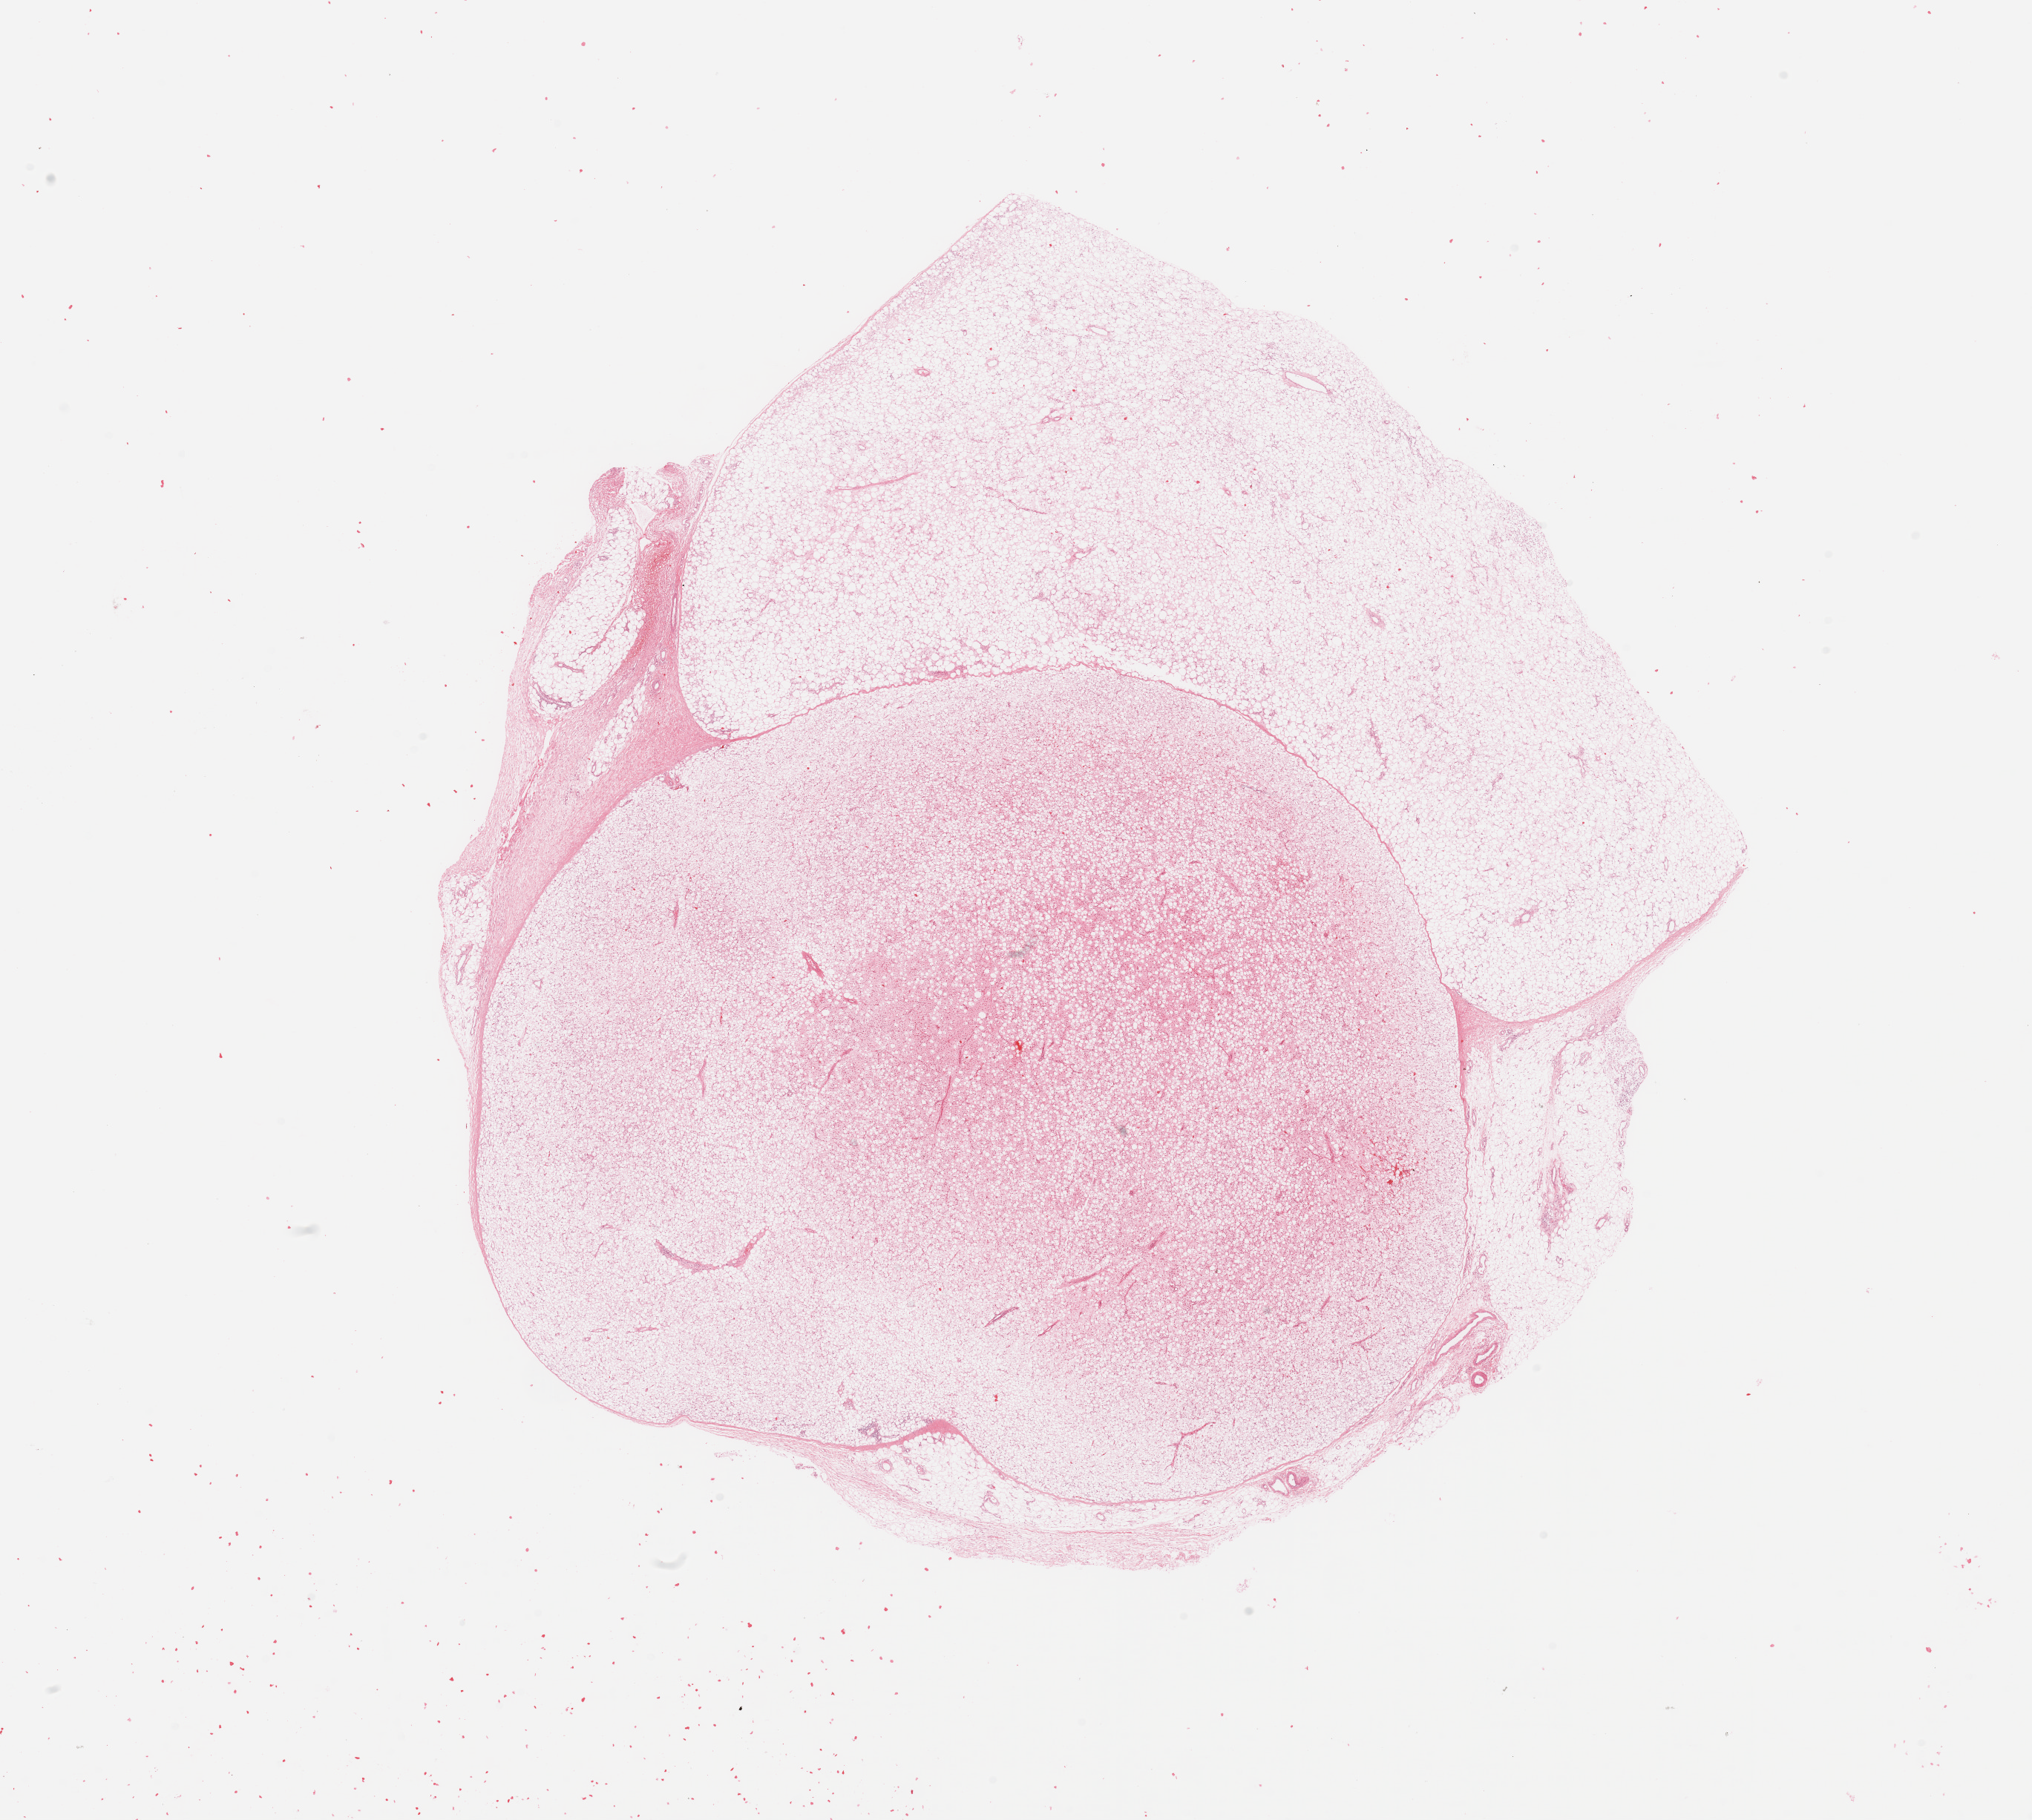
Hematoxylin and eosin (H&E) stained whole-slide image — a low-resolution overview of the entire scanned area, about 21.7 x 19.4 mm. Tumour tissue sample. Female, 32 y/o.
Primary tumour site (as recorded): lower extremity. Patient diagnosis (cohort enrolment): sarcoma (site not recorded at cohort level).